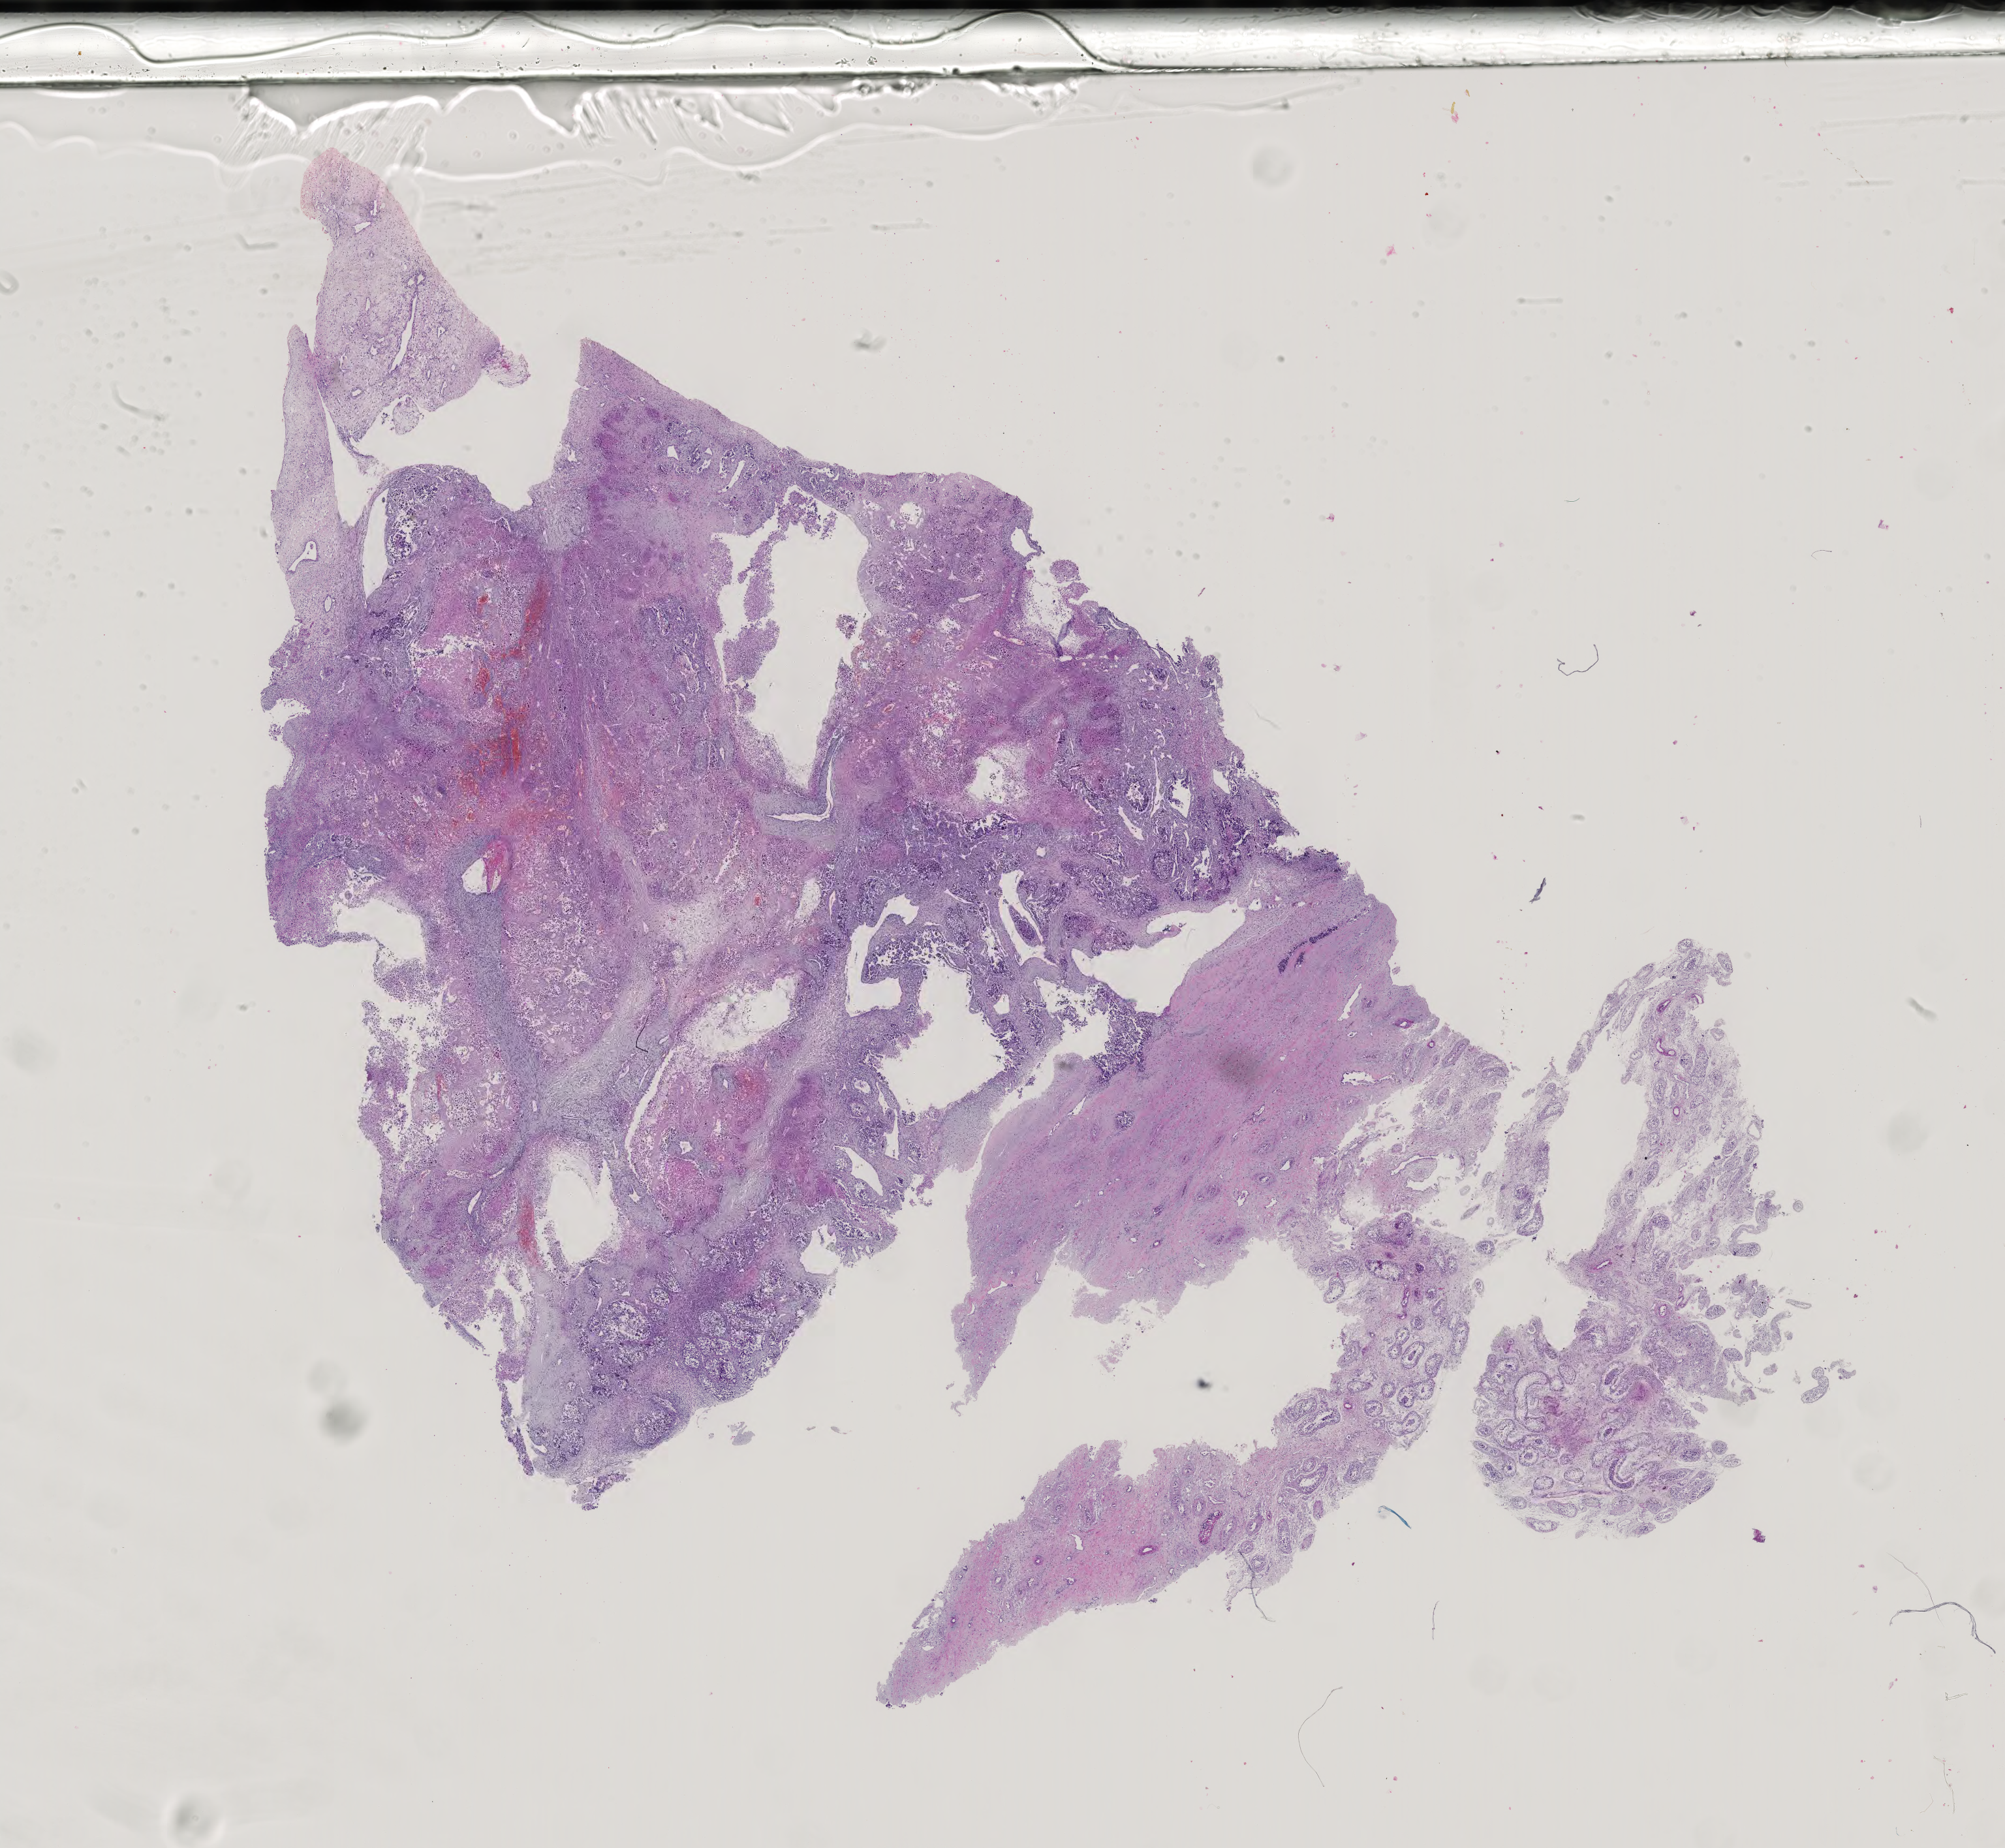
Digitized Hematoxylin and eosin (H&E) stained tissue section (whole slide) — whole scanned area (about 22.4 x 20.6 mm) shown as a low-resolution overview; formalin-fixed paraffin-embedded (FFPE) diagnostic section; sample: primary tumour, testis. Male patient; age at initial diagnosis 14 years.
Pathologic diagnosis: Mixed germ cell tumor. AJCC pathologic stage: II.